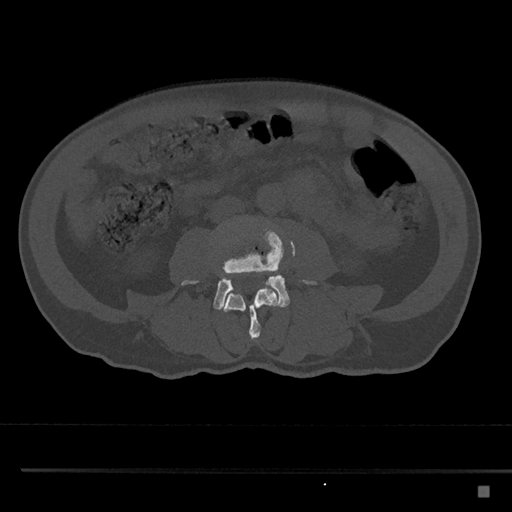
CT including the spine, one axial slice. Position 664 of 797 along the scan axis. Reconstruction kernel Br40s/3. 120 kVp. Bone window (W 1800 / L 400 HU). 512 × 512 image matrix, field of view 391 × 391 mm. Patient: male, 59 years. Case-level facts recorded for this patient, not image findings: primary cancer: prostate.
Outlined on this slice (semi-automatic segmentation, software-assisted and operator-edited):
- L3 vertebra: bounding box <222,284,280,341> (left, top, right, bottom; pixels)
- L4 vertebra: <181,224,318,310>